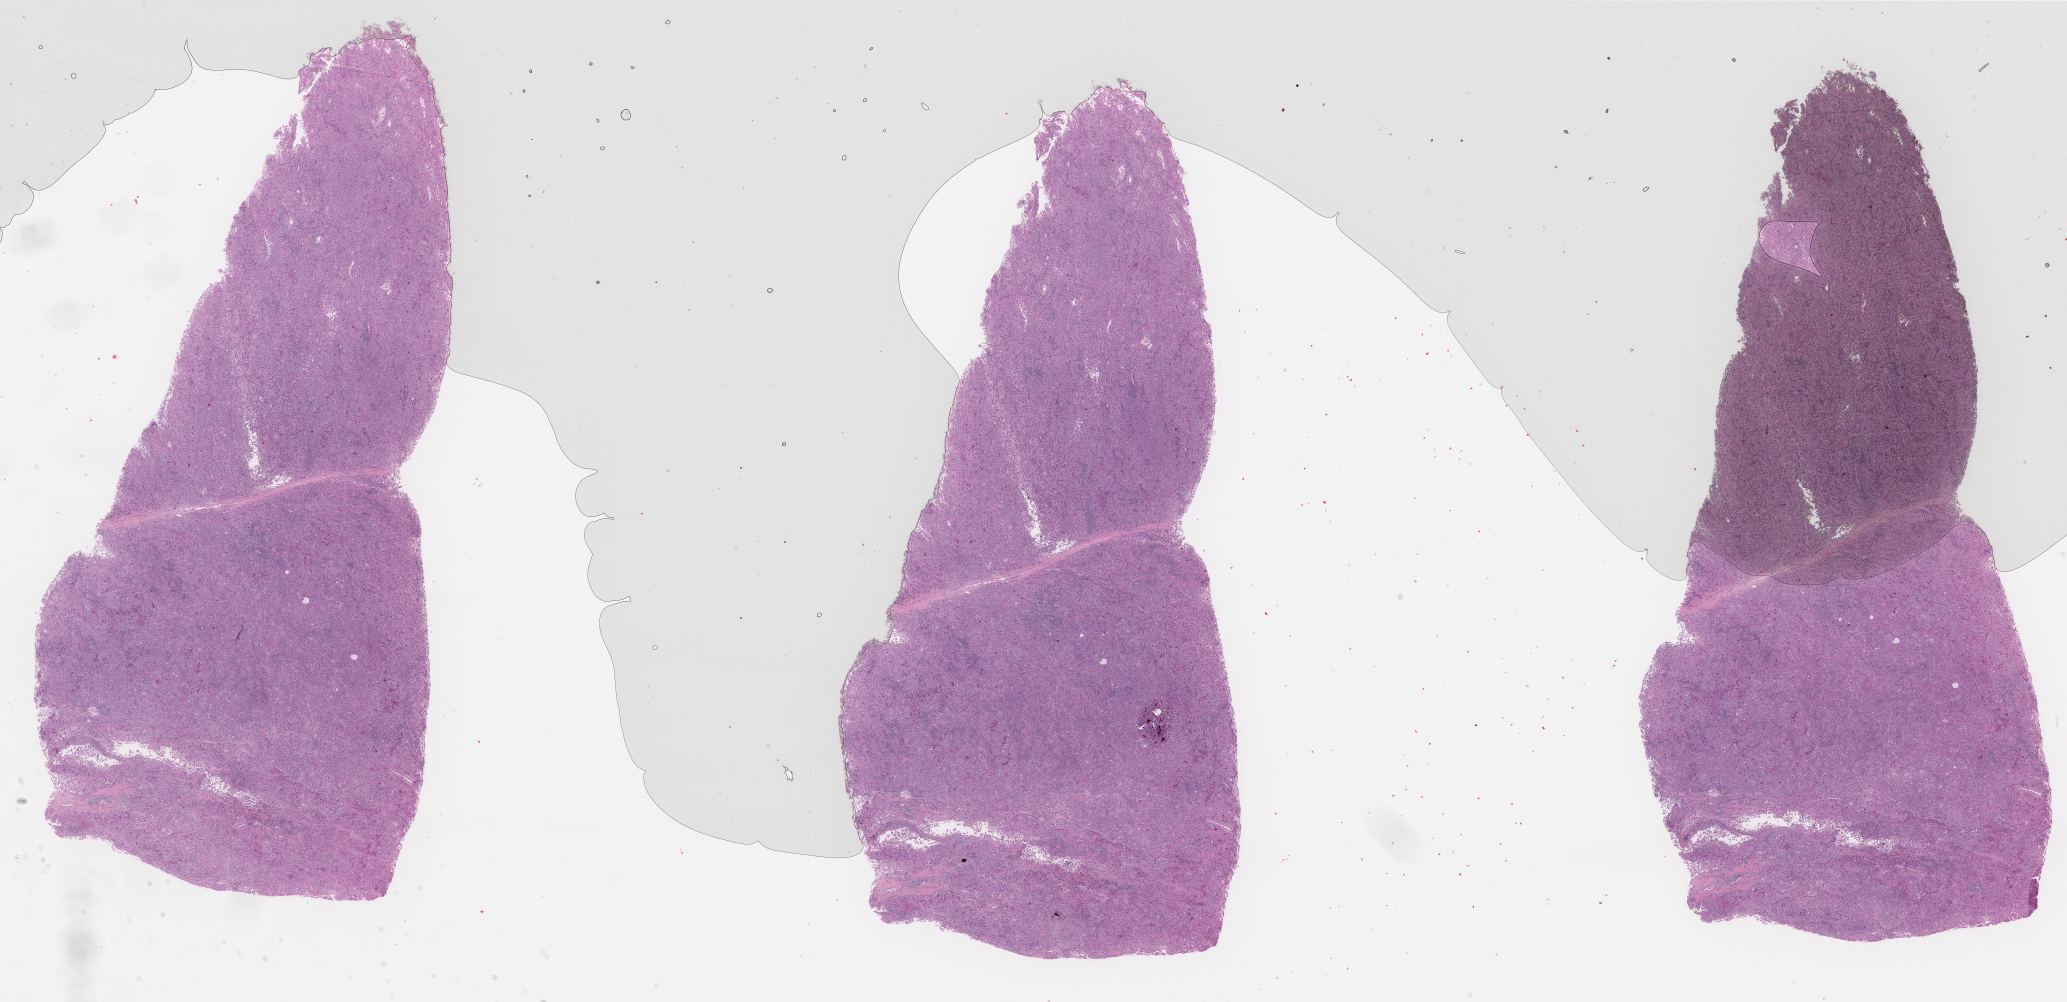
Whole-slide histology image, Hematoxylin and eosin (H&E) stained — low-resolution overview of the scanned area, about 32.7 x 15.9 mm (acquisition: 40x scan). Formalin-fixed paraffin-embedded (FFPE) diagnostic section. Sample: primary tumour, skin. Female, age 29 years at initial diagnosis.
* diagnosis: Malignant melanoma, NOS